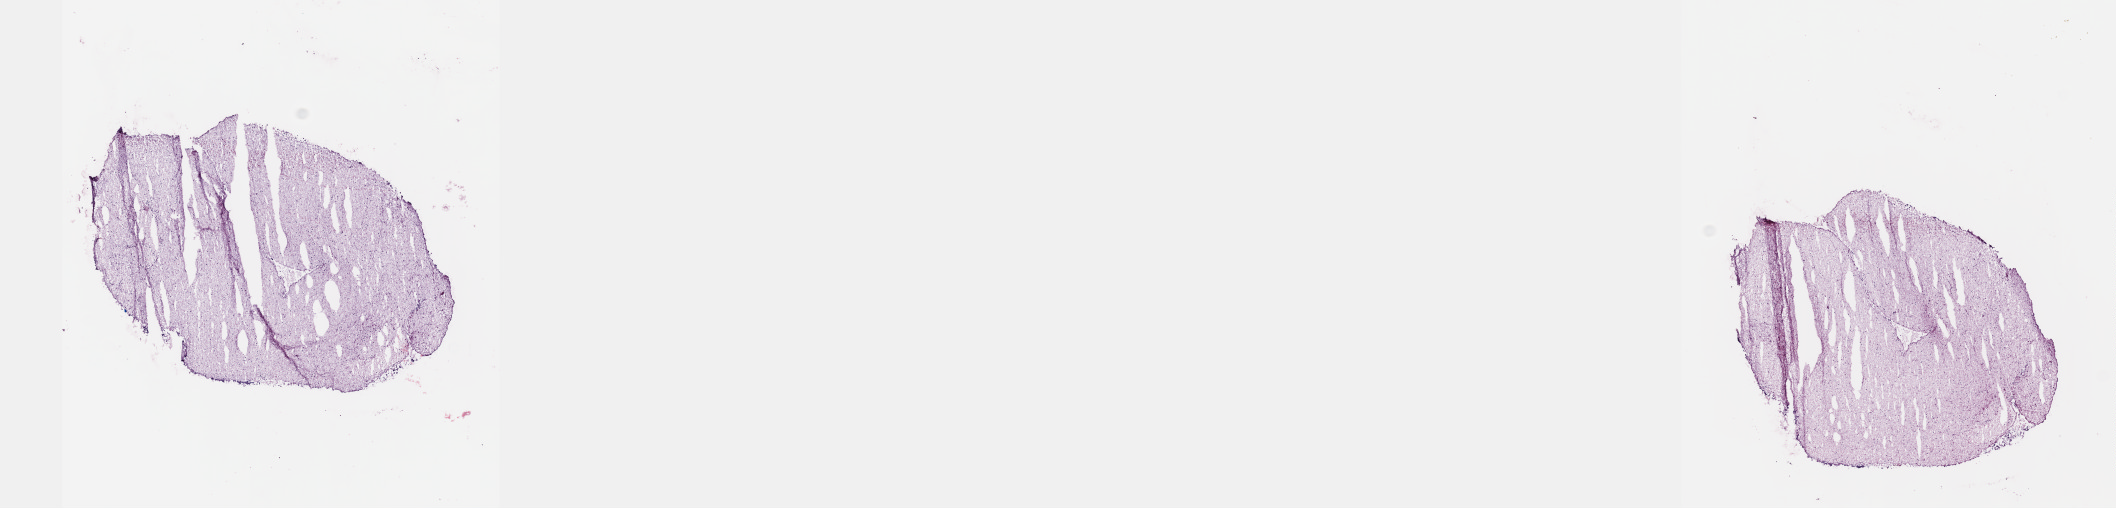
Digitized Hematoxylin and eosin (H&E) stained tissue section (whole slide), a low-resolution overview of the entire scanned area, about 17.1 x 4.1 mm (slide scanned at 40x). Frozen section. Primary tumour sample from the retroperitoneum and peritoneum. Male, age 56 years at initial diagnosis. Pathologist review of this section (percent, as recorded): tumour cells 100%, tumour nuclei 80%, normal cells 0%, stromal cells 0%, necrosis 0%. Infiltration values recorded for this section: lymphocyte infiltration 1%, monocyte infiltration 0%, neutrophil infiltration 0%.
Diagnosis: Extra-adrenal paraganglioma, NOS (retroperitoneum).